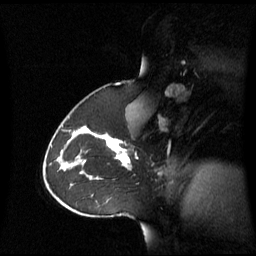
Breast MRI (dynamic contrast-enhanced), one sagittal slice. Slice 41 of 60 in the series (ordered by position). Dynamic contrast-enhanced series, image 2 of 3 at this slice position (ordered by acquisition). 1.5 T. TE 4.2 ms, TR 8.4 ms. 256 × 256 image matrix. Female patient, age 43 years. Case-level facts recorded for this patient, not image findings: setting: breast cancer imaged before/during neoadjuvant chemotherapy; receptor status: triple-negative.
Structures marked on this image (semi-automatically segmented with operator editing):
- analysis volume of interest (the breast-tissue region the enhancement analysis was run in; not a lesion): bounding box [x1, y1, x2, y2] px = [62, 124, 136, 180]
- tumour enhancement mask (voxels above the 70 % enhancement threshold inside the analysis volume of interest): [89, 133, 131, 166]